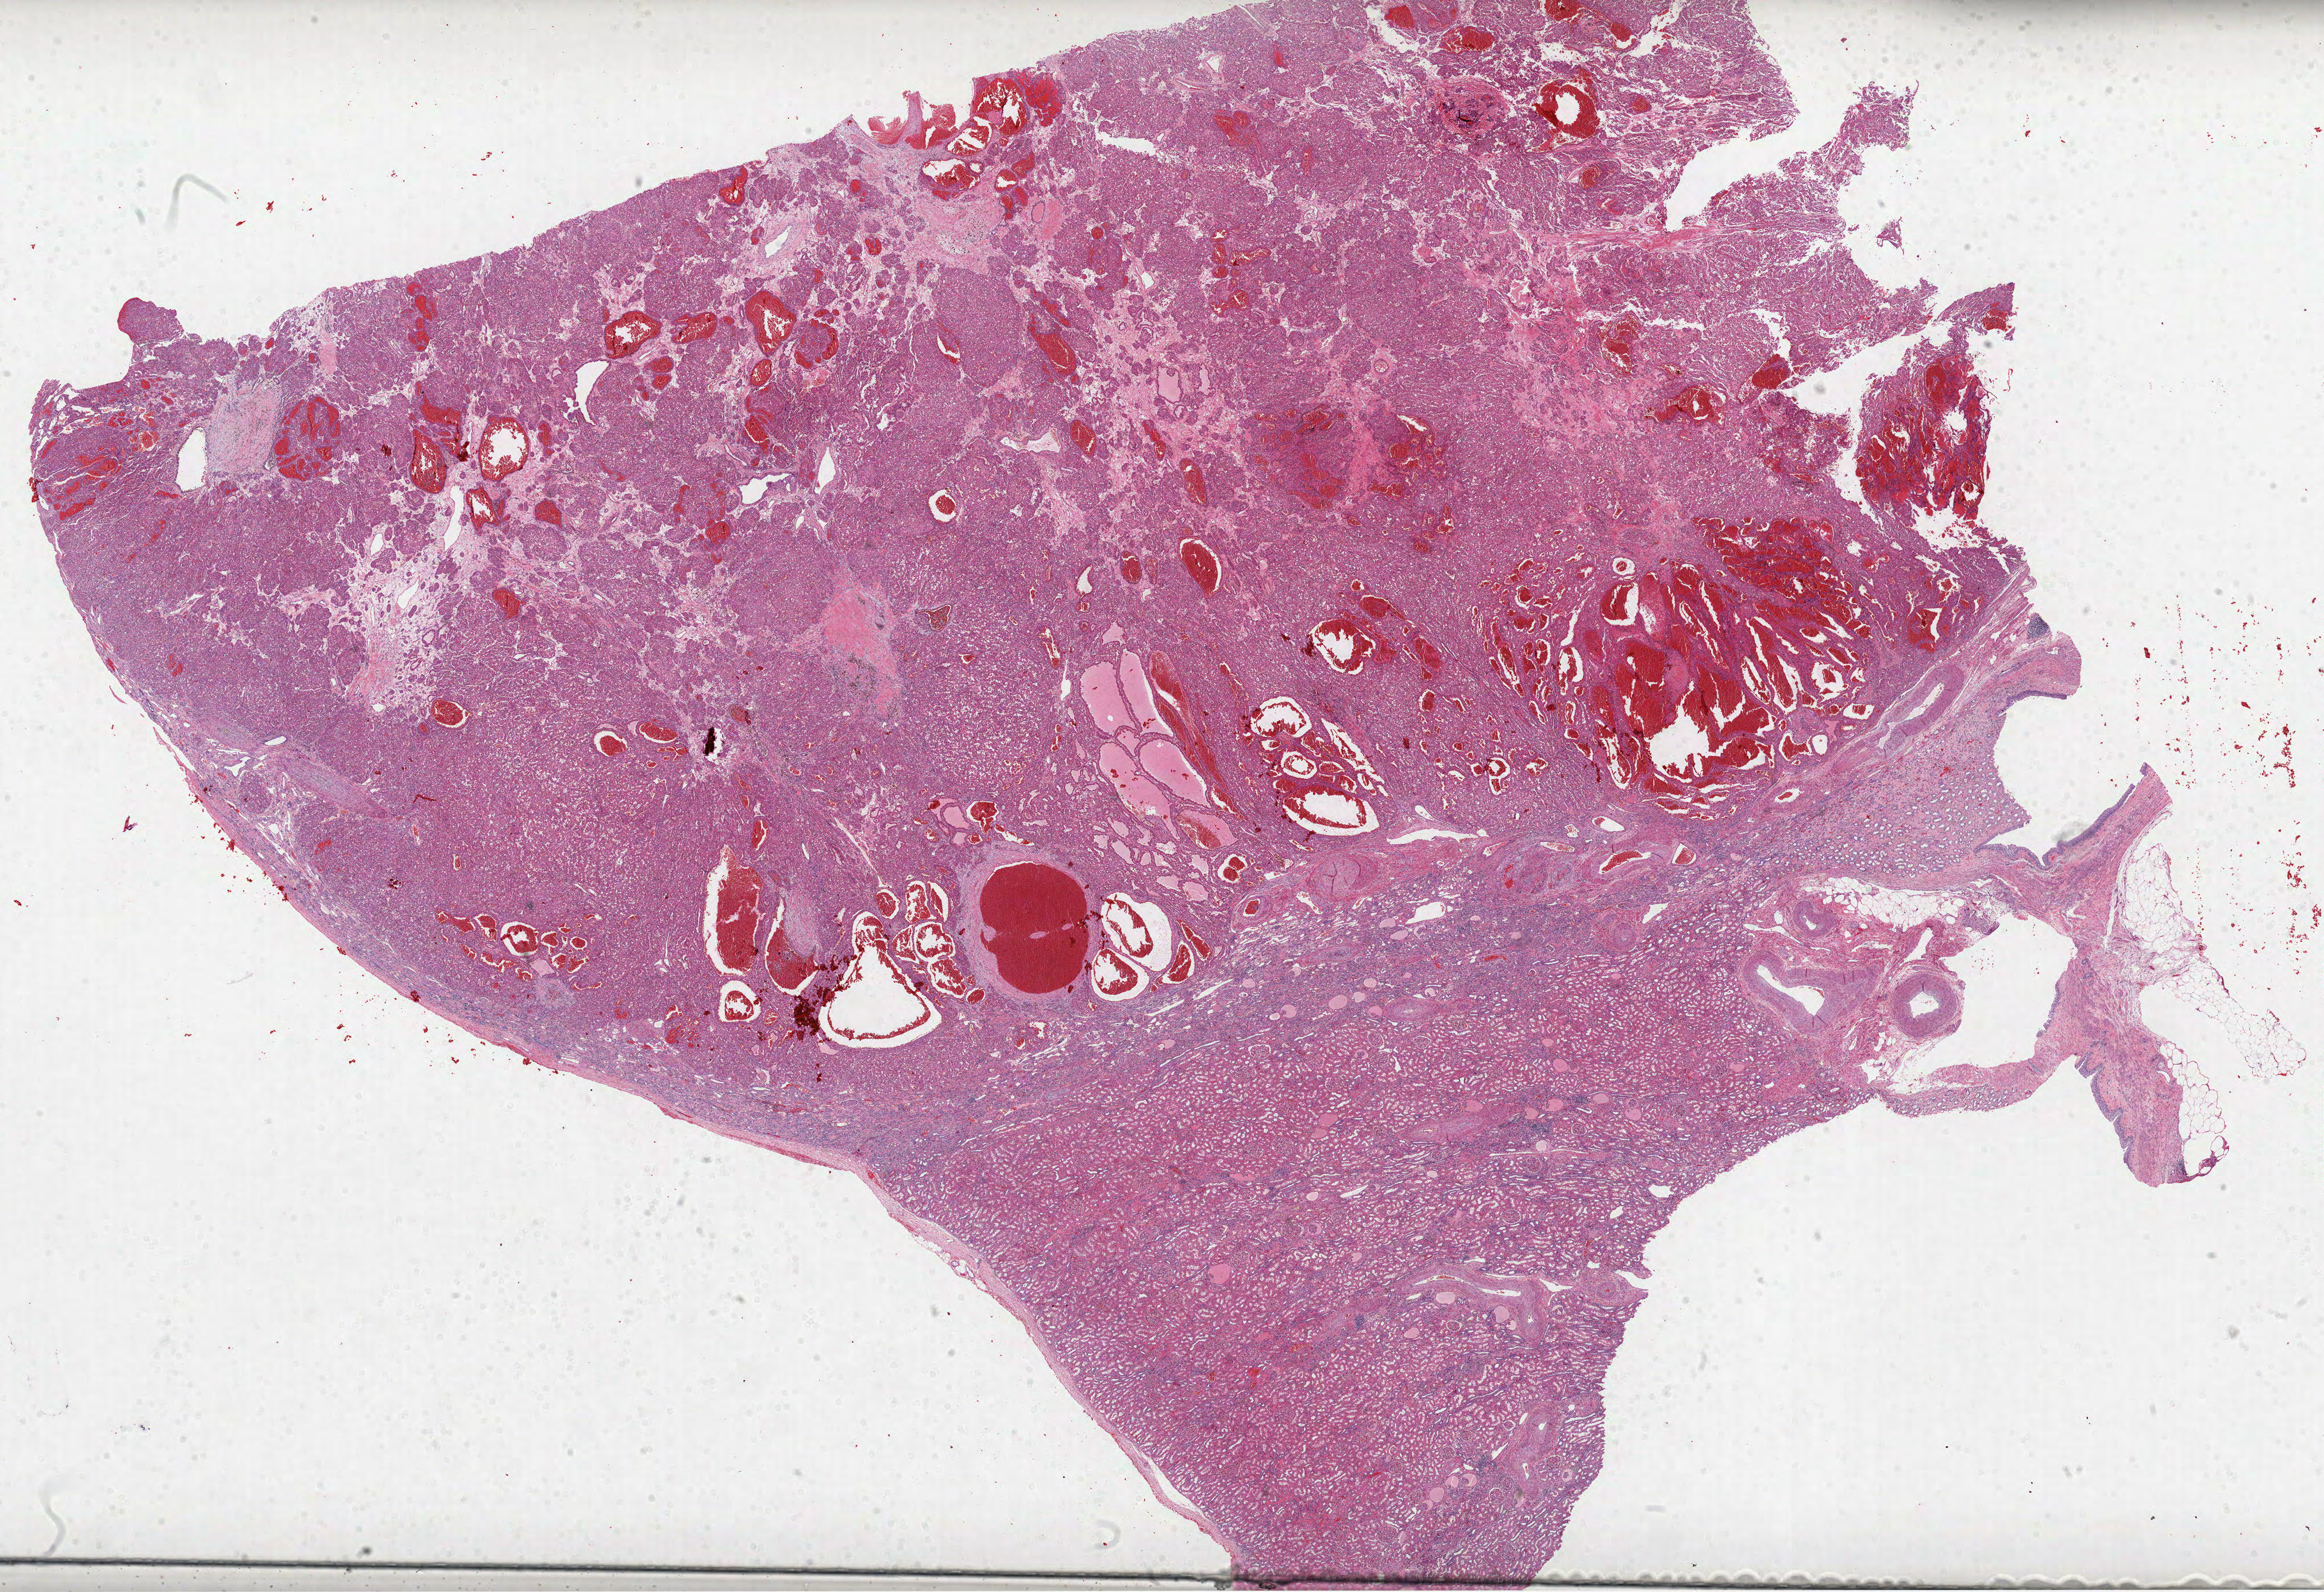
Whole-slide histology image, H&E-stained, a low-resolution overview of the entire scanned area, about 32.6 x 22.4 mm. Formalin-fixed paraffin-embedded (FFPE) diagnostic section. Primary tumour sample from the kidney. Patient: male, age at initial diagnosis 49 years. Histologic grade: G3 (poorly differentiated).
AJCC pathologic stage: I. Diagnosis: Clear cell adenocarcinoma, NOS.